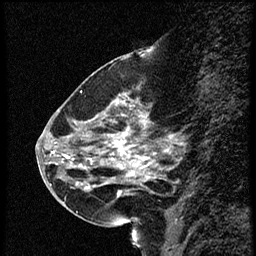
Breast MRI (dynamic contrast-enhanced), one sagittal slice. Position 22 of 56 along the scan axis. Dynamic contrast-enhanced study with each time point stored as its own series, time point 2 of 4 at this slice position (early post-contrast, ordered by acquisition time). 1.5 T. TE 4.2 ms, TR 18.9 ms. 2 mm slice thickness. 256 × 256 image matrix, field of view 200 × 200 mm. Female patient. Case-level facts recorded for this patient, not image findings: setting: breast cancer imaged before/during neoadjuvant chemotherapy; receptor status: HER2-positive.
Outlined on this slice (semi-automatically segmented with operator editing):
- analysis volume of interest (the breast-tissue region the enhancement analysis was run in; not a lesion): bounding box <63,80,169,215> (left, top, right, bottom; pixels)
- tumour enhancement mask (voxels above the 100 % enhancement threshold inside the analysis volume of interest): <77,90,149,197>